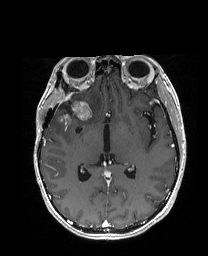
Brain MRI from a brain-tumour surgery series, one axial slice. Position 97 of 192 along the scan axis. T1-weighted post-contrast. 1 mm slice thickness. 208 × 256 image matrix, field of view 203 × 250 mm. Case-level facts recorded for this patient, not image findings: histopathology: Metastatic Carcinoma from Breast primary.
Structures marked on this image (outlined manually by an expert reader):
- previous resection cavity: bounding box [x1, y1, x2, y2] px = [60, 104, 71, 113]
- tumour: [55, 99, 104, 123]